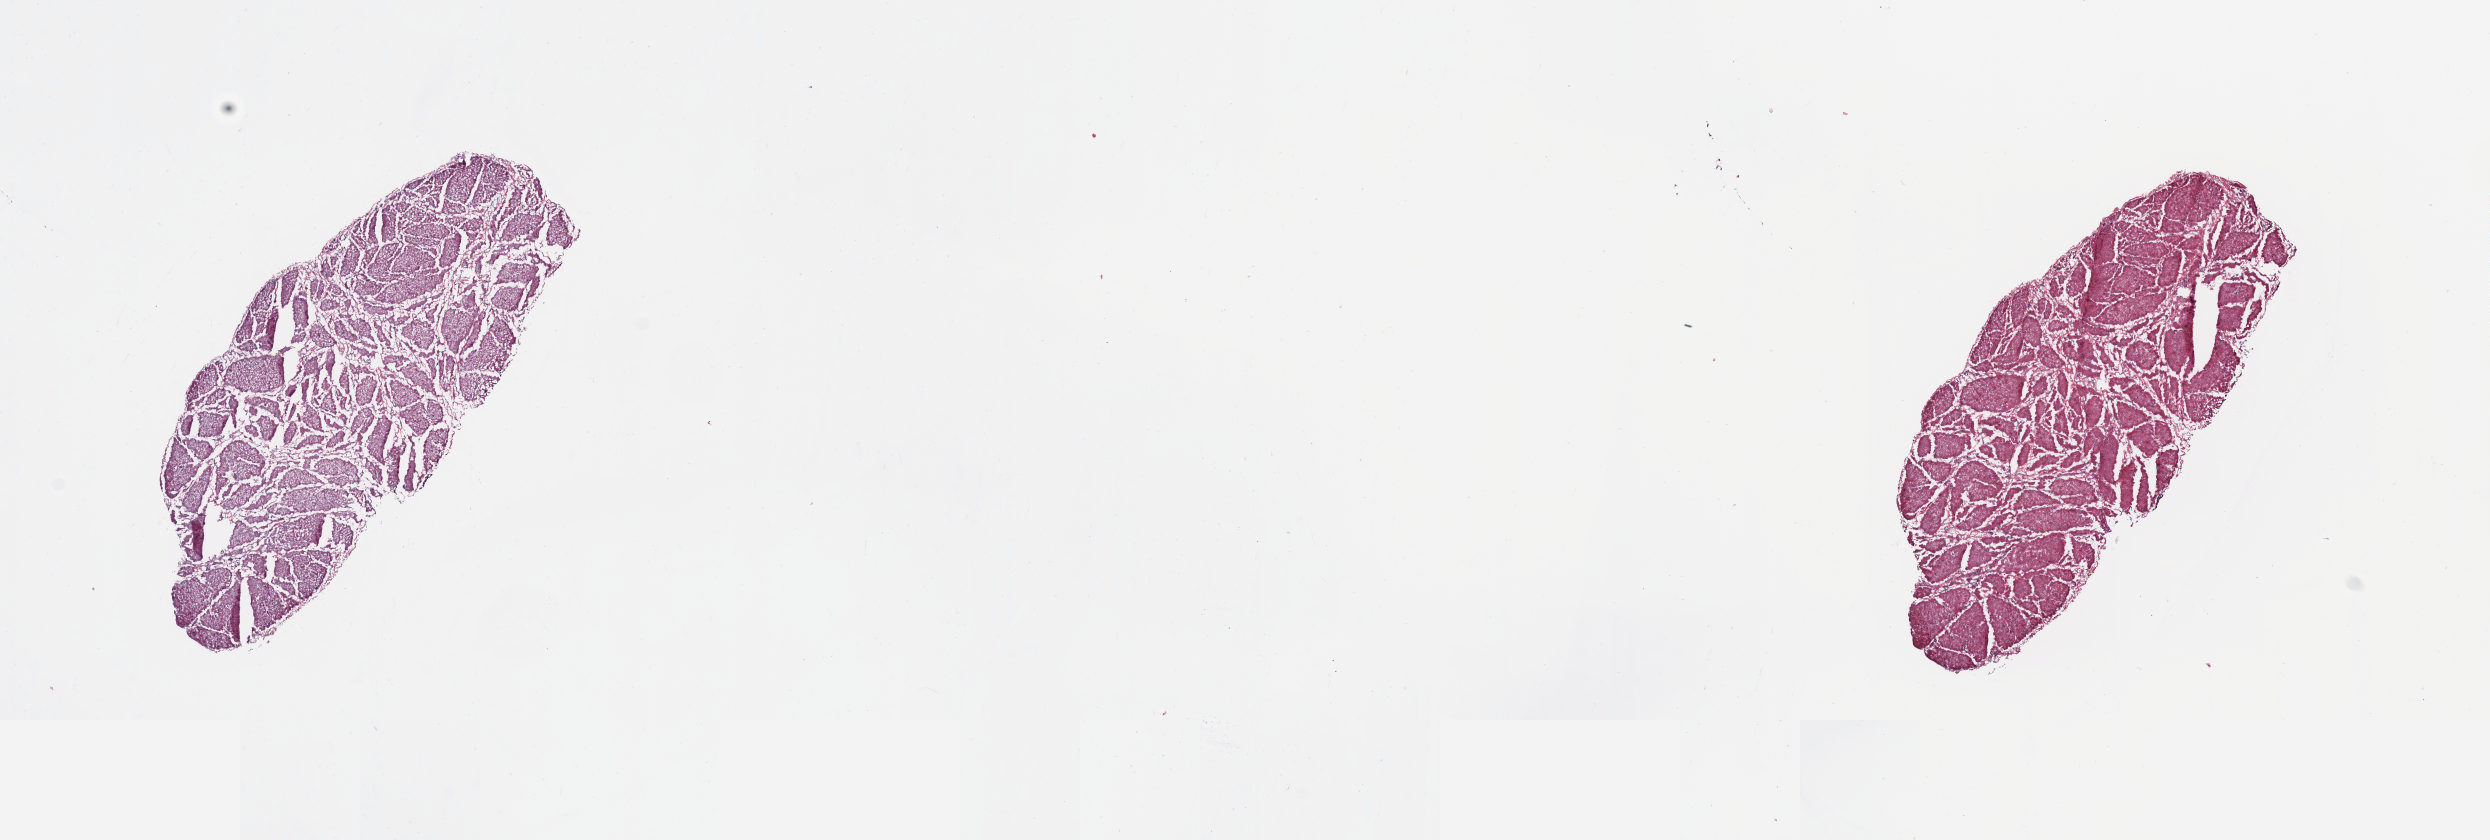
Digitized Hematoxylin and eosin (H&E) stained tissue section (whole slide) — a low-resolution overview of the entire scanned area, about 19.7 x 6.6 mm; frozen section; sample: solid tissue normal (non-tumour tissue), stomach. Patient: female, age at initial diagnosis 76 years. Slide review estimates, as recorded: tumour cells 0%, tumour nuclei 0%, normal cells 0%, stromal cells 100%, necrosis 0%. Infiltration values recorded for this section: lymphocyte infiltration 1%, monocyte infiltration 0%, neutrophil infiltration 0%.
This section: solid tissue normal (non-tumour) sample from the same patient. Patient diagnosis: Carcinoma, diffuse type (gastric antrum).